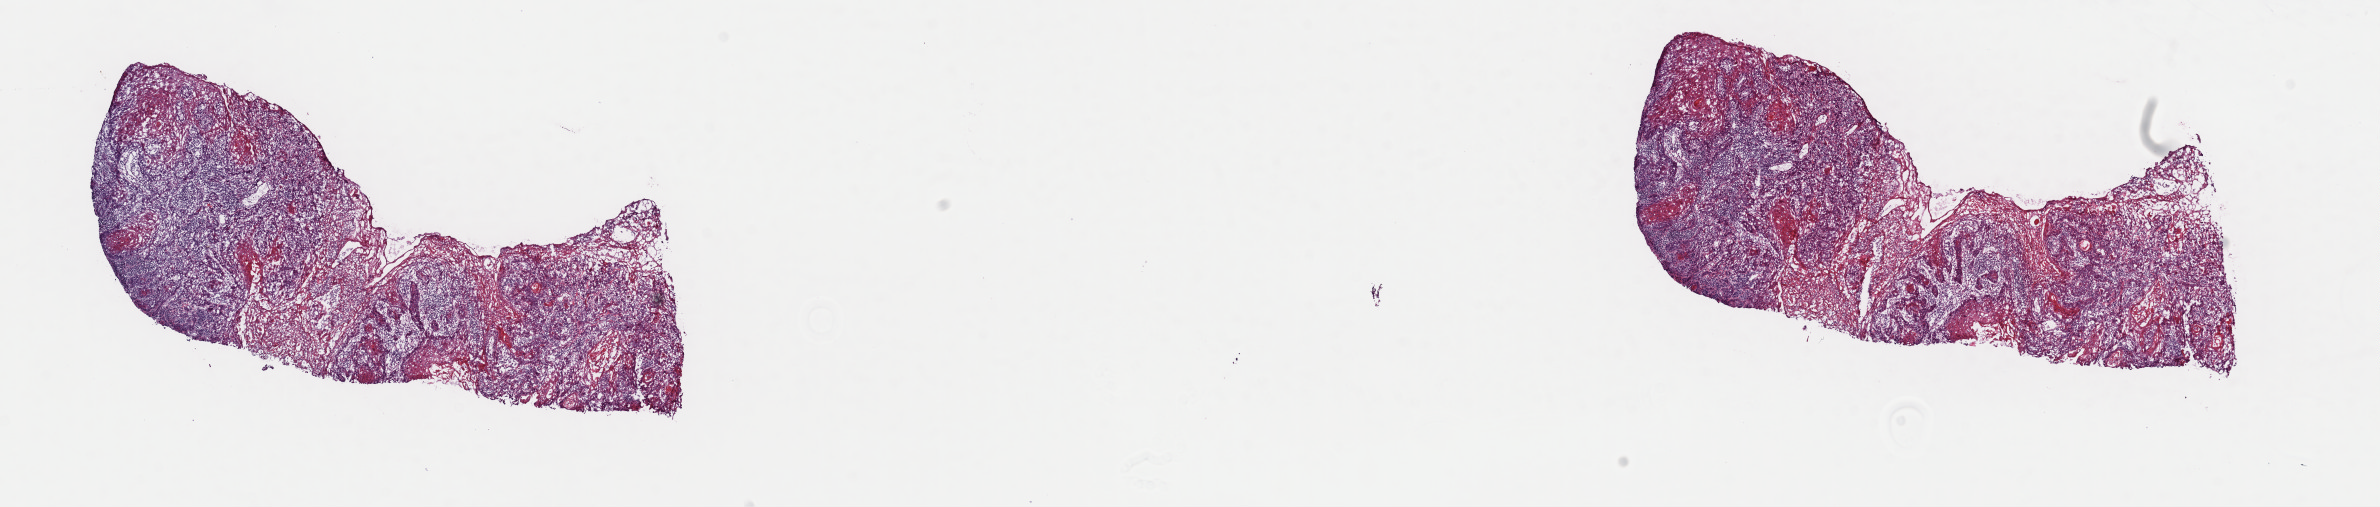
Hematoxylin and eosin (H&E) stained whole-slide image — whole scanned area (about 18.8 x 4.0 mm, acquisition: 40x scan) shown as a low-resolution overview; frozen section from the top of the tissue portion; sample: primary tumour, head and neck. Male, age 47 years at initial diagnosis. Histologic grade: G1 (well differentiated). Composition of this section per pathologist review: tumour cells 100%, tumour nuclei 80%, normal cells 0%, stromal cells 0%, necrosis 0%. Infiltration values recorded for this section: lymphocyte infiltration 2%, monocyte infiltration 0%, neutrophil infiltration 0%.
Lymph nodes positive (case pathology): 1 of 12 examined. AJCC pathologic stage: III (7th edition). Histologic diagnosis: Squamous cell carcinoma, keratinizing, NOS (base of tongue, NOS).